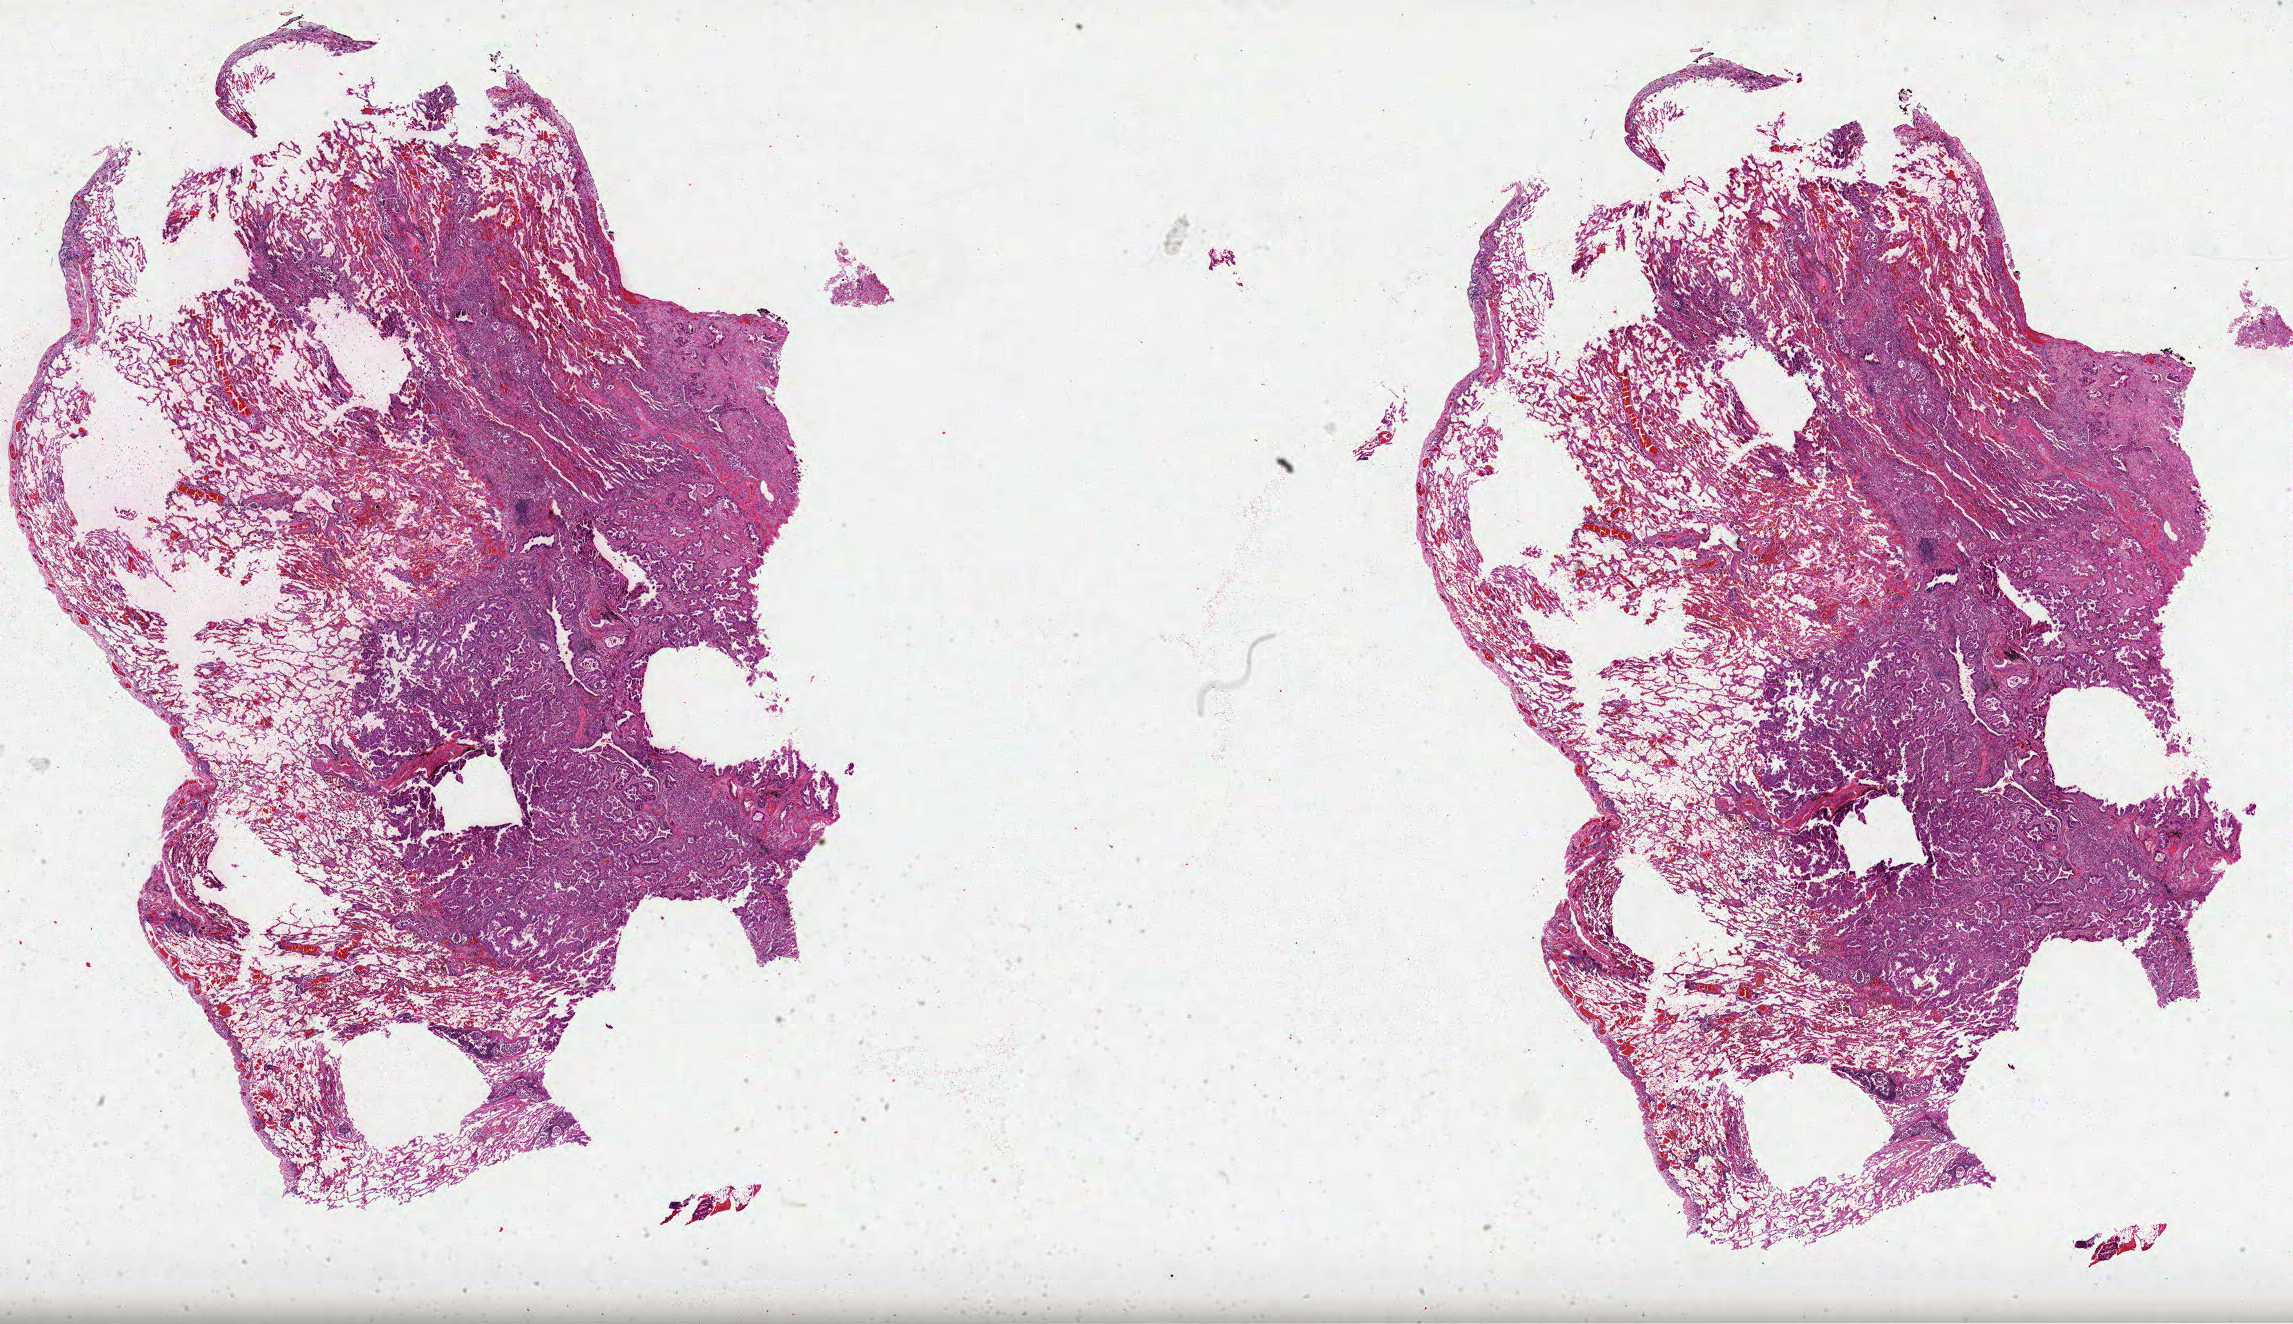
Hematoxylin and eosin (H&E) stained whole-slide image, low-resolution overview of the scanned area, about 37.0 x 21.4 mm. Formalin-fixed paraffin-embedded (FFPE) diagnostic section. Primary tumour sample from the lung. Female, age 45 years at initial diagnosis.
Pathologic diagnosis: Adenocarcinoma, NOS (upper lobe, lung). AJCC pathologic stage: IIIA (4th edition). Laterality: left.